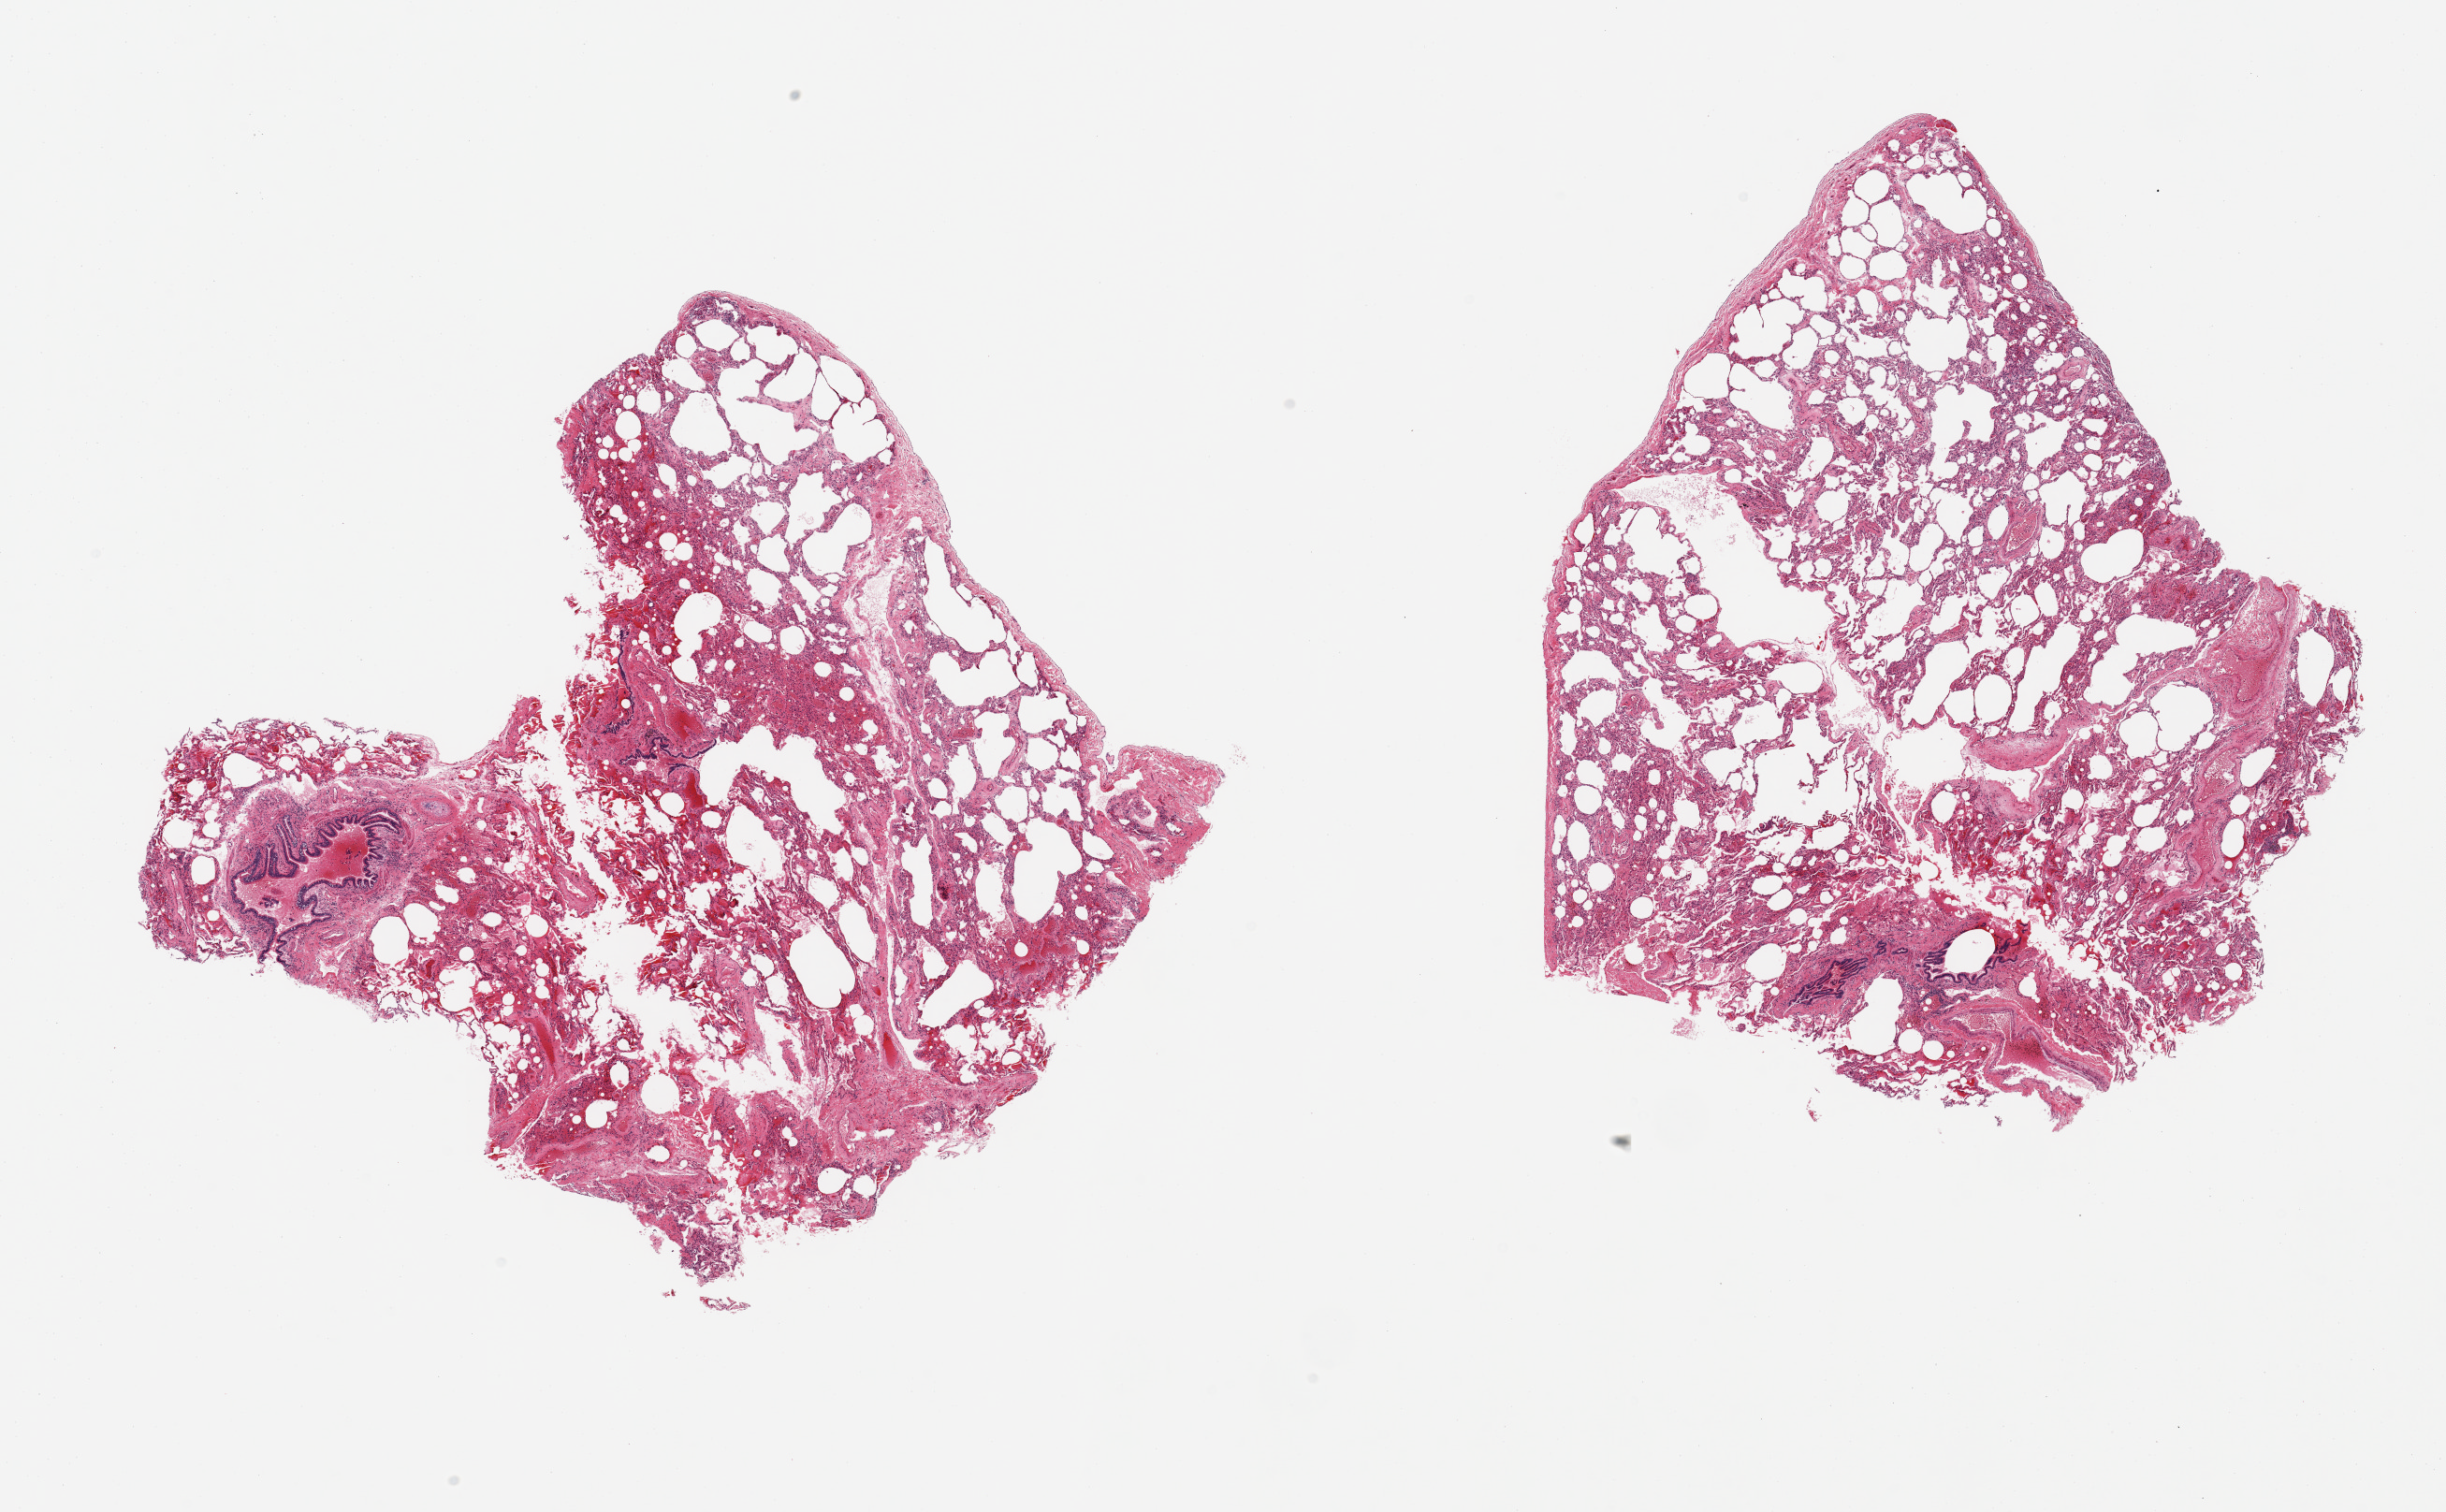
Hematoxylin and eosin (H&E) whole-slide image — a low-resolution overview of the entire scanned area, about 20.7 x 12.8 mm, PAXgene-fixed, paraffin-embedded tissue, section of lung (target tissue), donor tissue sample. Donor sex: female.
* reviewer comment on this tissue sample: 2 pieces; moderate emphysema; mild patchy alveolar hemorrhage